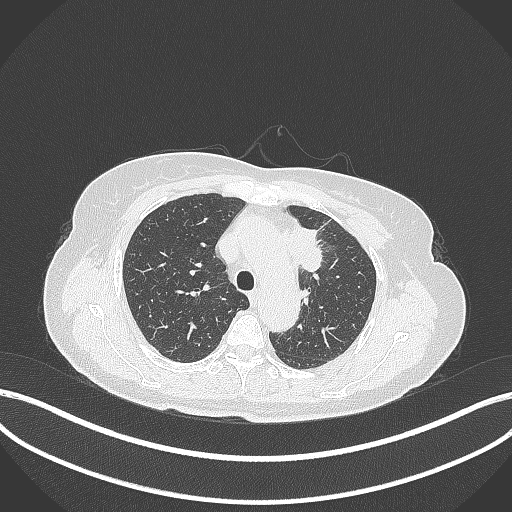
Chest CT, one axial slice. Slice 245 of 369 in the series (ordered by position). Reconstruction kernel B70f. 120 kVp. Lung window (W 1500 / L -600 HU). 1 mm slice thickness. 512 × 512 image matrix, field of view 400 × 400 mm. Female patient, age 65 years. From the clinical record (not read from this slice): clinical TNM (as recorded): T2a N0 M0.
Annotated regions visible in this slice (bounding box drawn by a radiologist):
- lung tumour (recorded histology: adenocarcinoma): box from (x=284, y=222) to (x=325, y=273) px